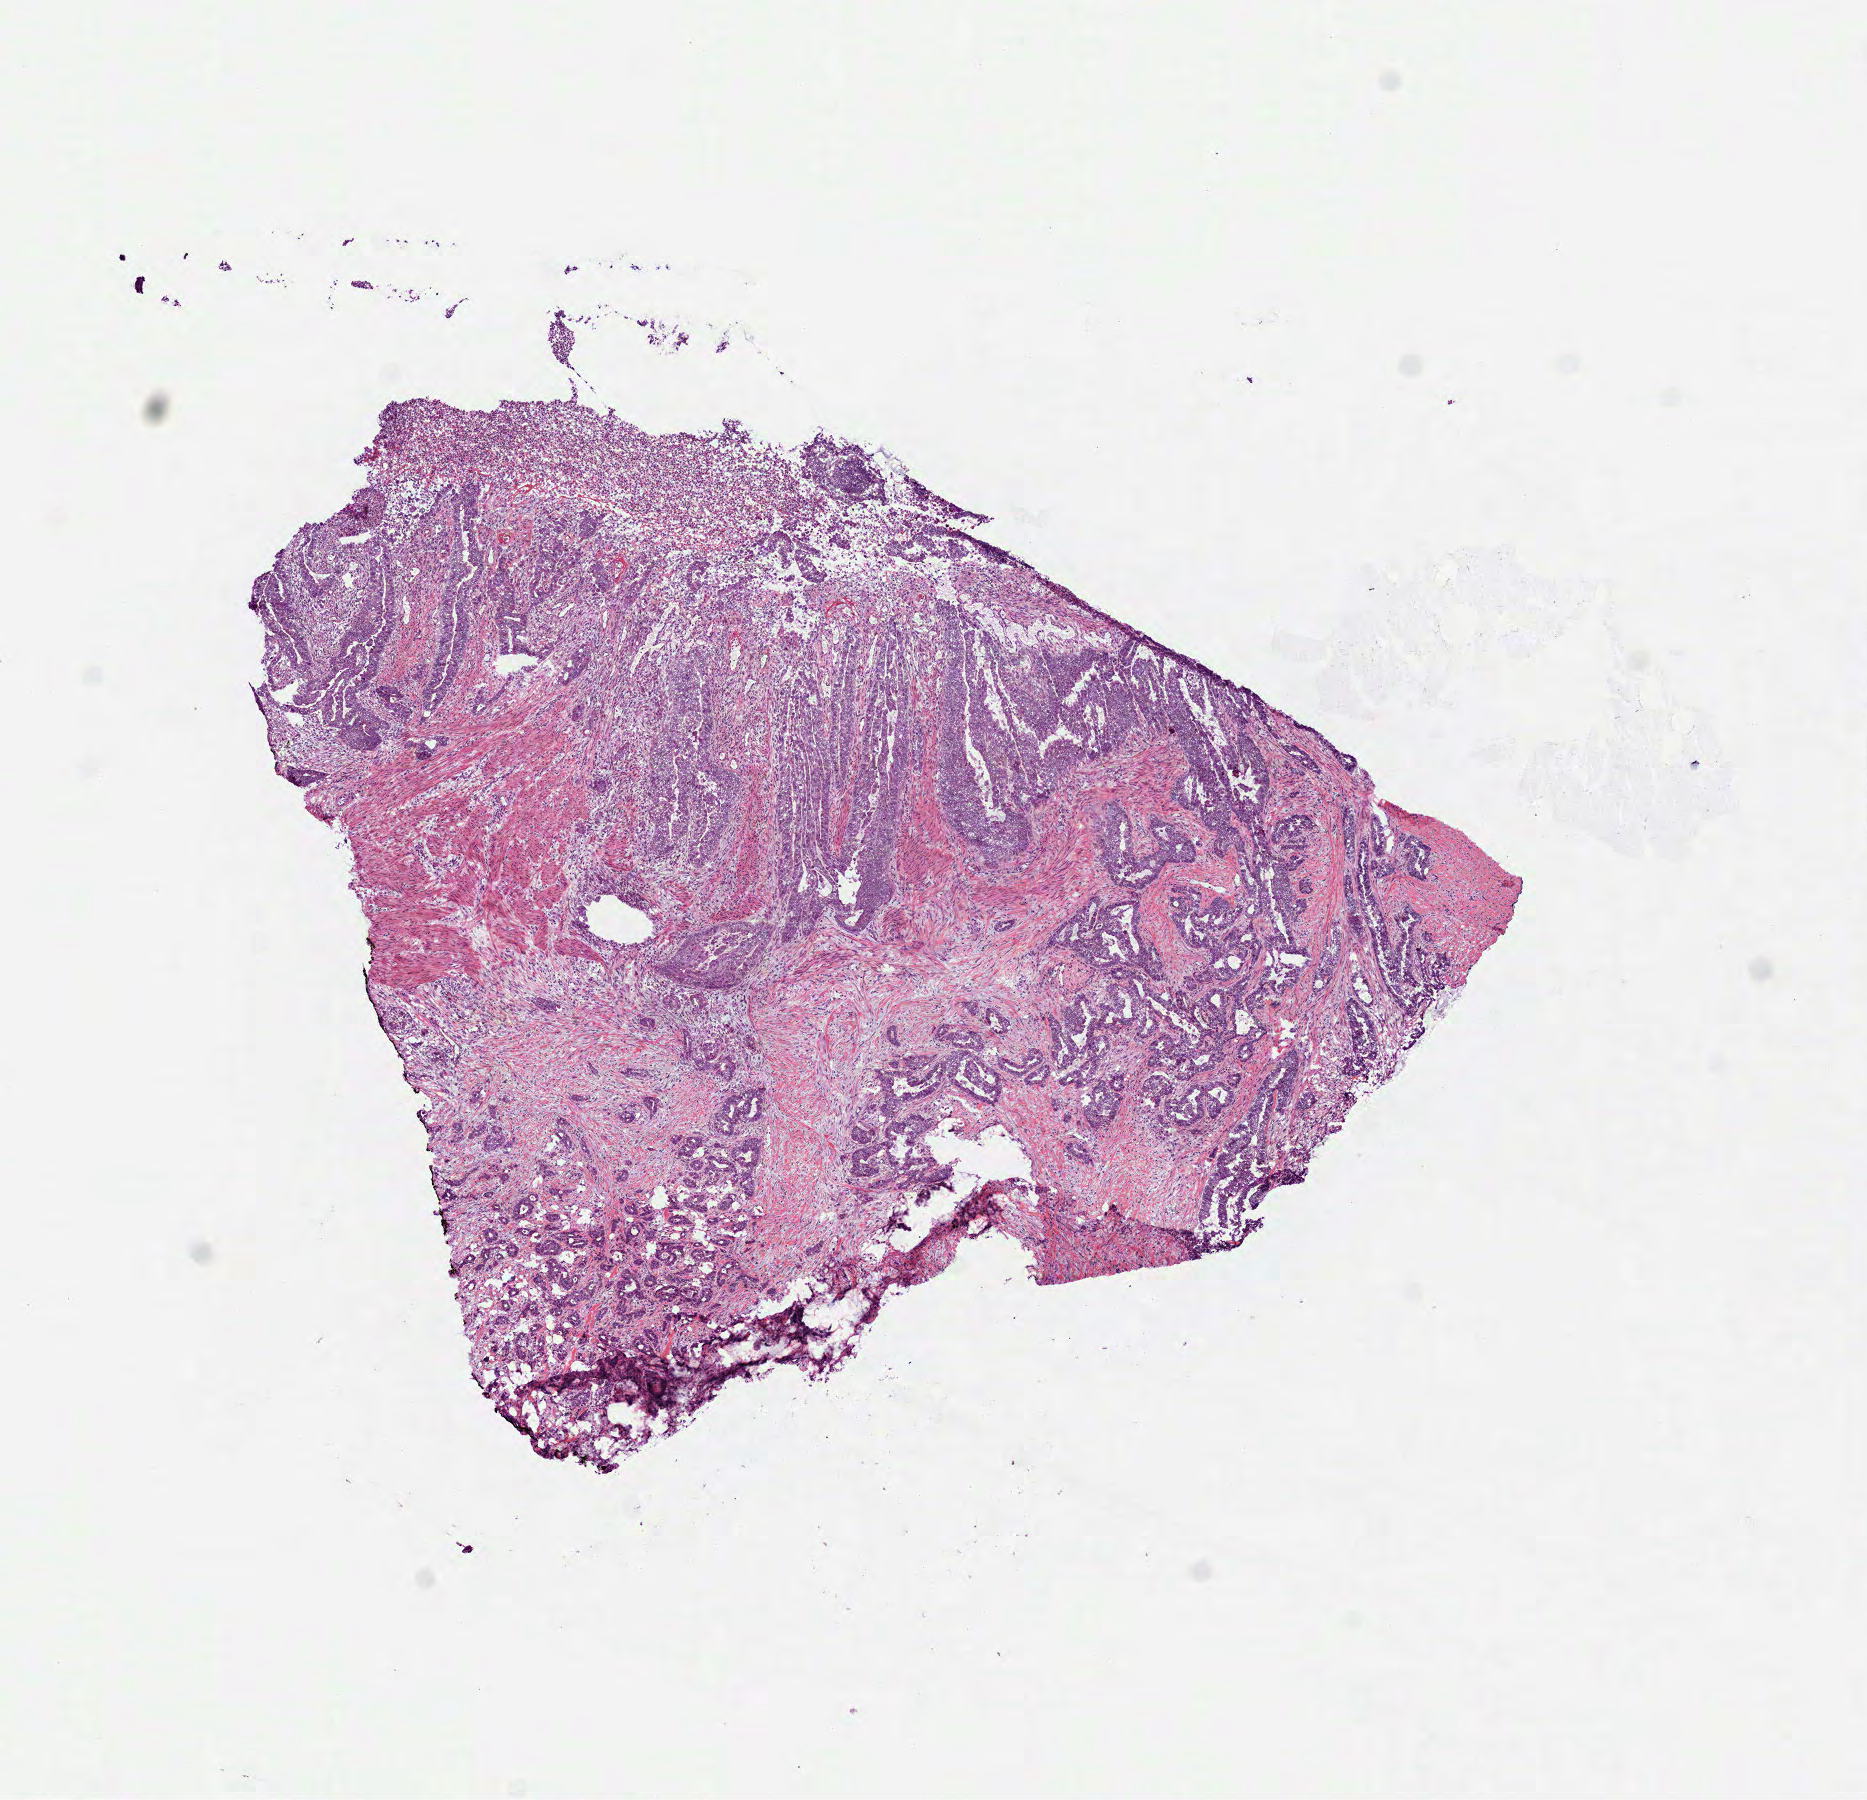
H&E-stained whole-slide image — shown as a low-resolution overview of the whole scanned area (about 7.5 x 7.3 mm, acquisition: 40x scan), frozen section, colon, primary tumour sample. Patient: female, age at initial diagnosis 56 years. Composition of this section per pathologist review: tumour cells 99%, tumour nuclei 80%, normal cells 0%, stromal cells 0%, necrosis 1%. Inflammatory infiltration, as recorded: lymphocyte infiltration 5%, monocyte infiltration 0%, neutrophil infiltration 2%.
- AJCC pathologic stage: IVA (7th edition)
- histologic diagnosis: Adenocarcinoma, NOS (sigmoid colon)
- lymph nodes positive (case pathology): 1 of 37 examined